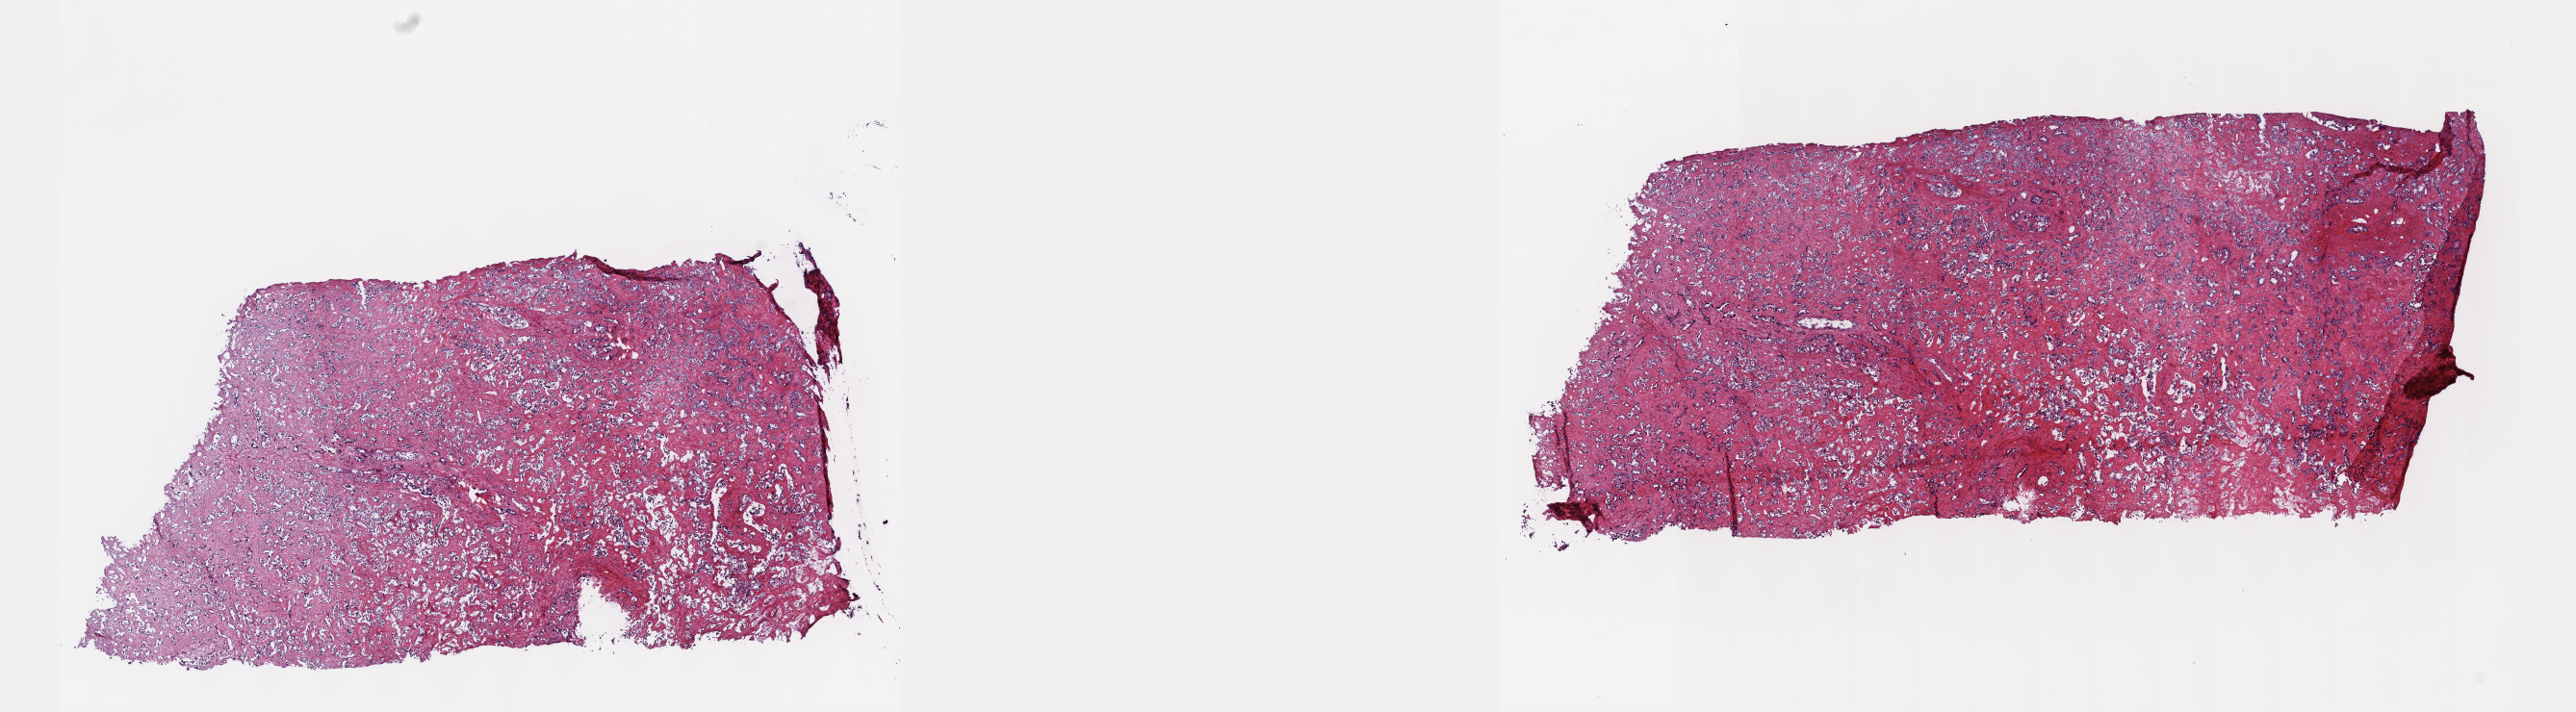
H&E-stained whole-slide image, shown as a low-resolution overview of the whole scanned area (about 21.6 x 6.0 mm, acquisition: 40x scan), frozen section from the top of the tissue portion, bile duct, primary tumour sample. Patient: female, age at initial diagnosis 46 years. Histologic grade: G2 (moderately differentiated). Slide review estimates, as recorded: tumour cells 100%, tumour nuclei 65%, normal cells 0%, stromal cells 0%, necrosis 0%. Infiltration values recorded for this section: lymphocyte infiltration 2%, monocyte infiltration 0%, neutrophil infiltration 0%.
AJCC pathologic stage: I. Diagnosis: Cholangiocarcinoma.